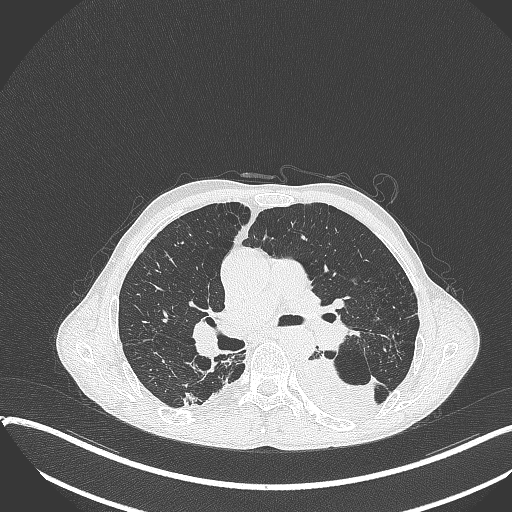
Chest CT, one axial slice; slice 227 of 401 in the series (ordered by position); lung window (W 1500 / L -600 HU); 512 × 512 image matrix, field of view 400 × 400 mm. Patient: male, 57 years. From the clinical record (not read from this slice): clinical TNM (as recorded): T4 N0 M0.
Outlined on this slice (bounding box drawn by a radiologist):
- lung tumour (recorded histology: squamous cell carcinoma): box from (x=292, y=353) to (x=377, y=420) px